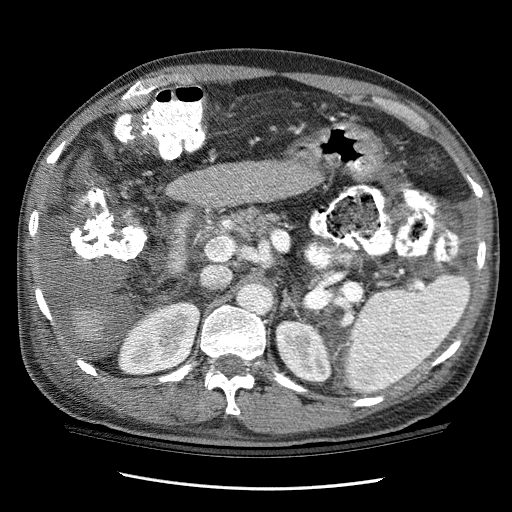
Contrast-enhanced abdominal CT (liver protocol), one axial slice. Slice 55 of 114 in the series (ordered by position). Reconstruction kernel STANDARD. One of 3 acquisitions stored at this slice position. Soft-tissue window (W 400 / L 40 HU). 512 × 512 image matrix. Case-level facts recorded for this patient, not image findings: diagnosis: hepatocellular carcinoma (patient treated with transarterial chemoembolisation; whether this scan precedes or follows treatment is not stated here); TNM stage (as recorded): Stage-I; Child-Pugh class: C.
Annotated regions visible in this slice (semi-automatic segmentation, software-assisted and operator-edited):
- liver parenchyma outside the tumour (the mass and vessels are separate outlines, so this box may not span the whole liver): bounding box (x1, y1, x2, y2) in pixels: (71, 157, 320, 340)